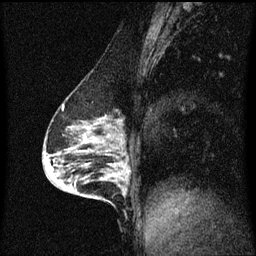
Breast MRI (dynamic contrast-enhanced), one sagittal slice; position 28 of 60 along the scan axis; dynamic contrast-enhanced series, image 2 of 3 at this slice position (ordered by acquisition); 1.5 T; TE 4.2 ms, TR 8.4 ms; 256 × 256 image matrix. Female patient, age 64 years.
Annotated regions visible in this slice (semi-automatic segmentation, software-assisted and operator-edited):
- analysis volume of interest (the breast-tissue region the enhancement analysis was run in; not a lesion): bounding box (x1, y1, x2, y2) in pixels: (90, 164, 129, 203)
- tumour enhancement mask (voxels above the 70 % enhancement threshold inside the analysis volume of interest): (122, 168, 129, 175)